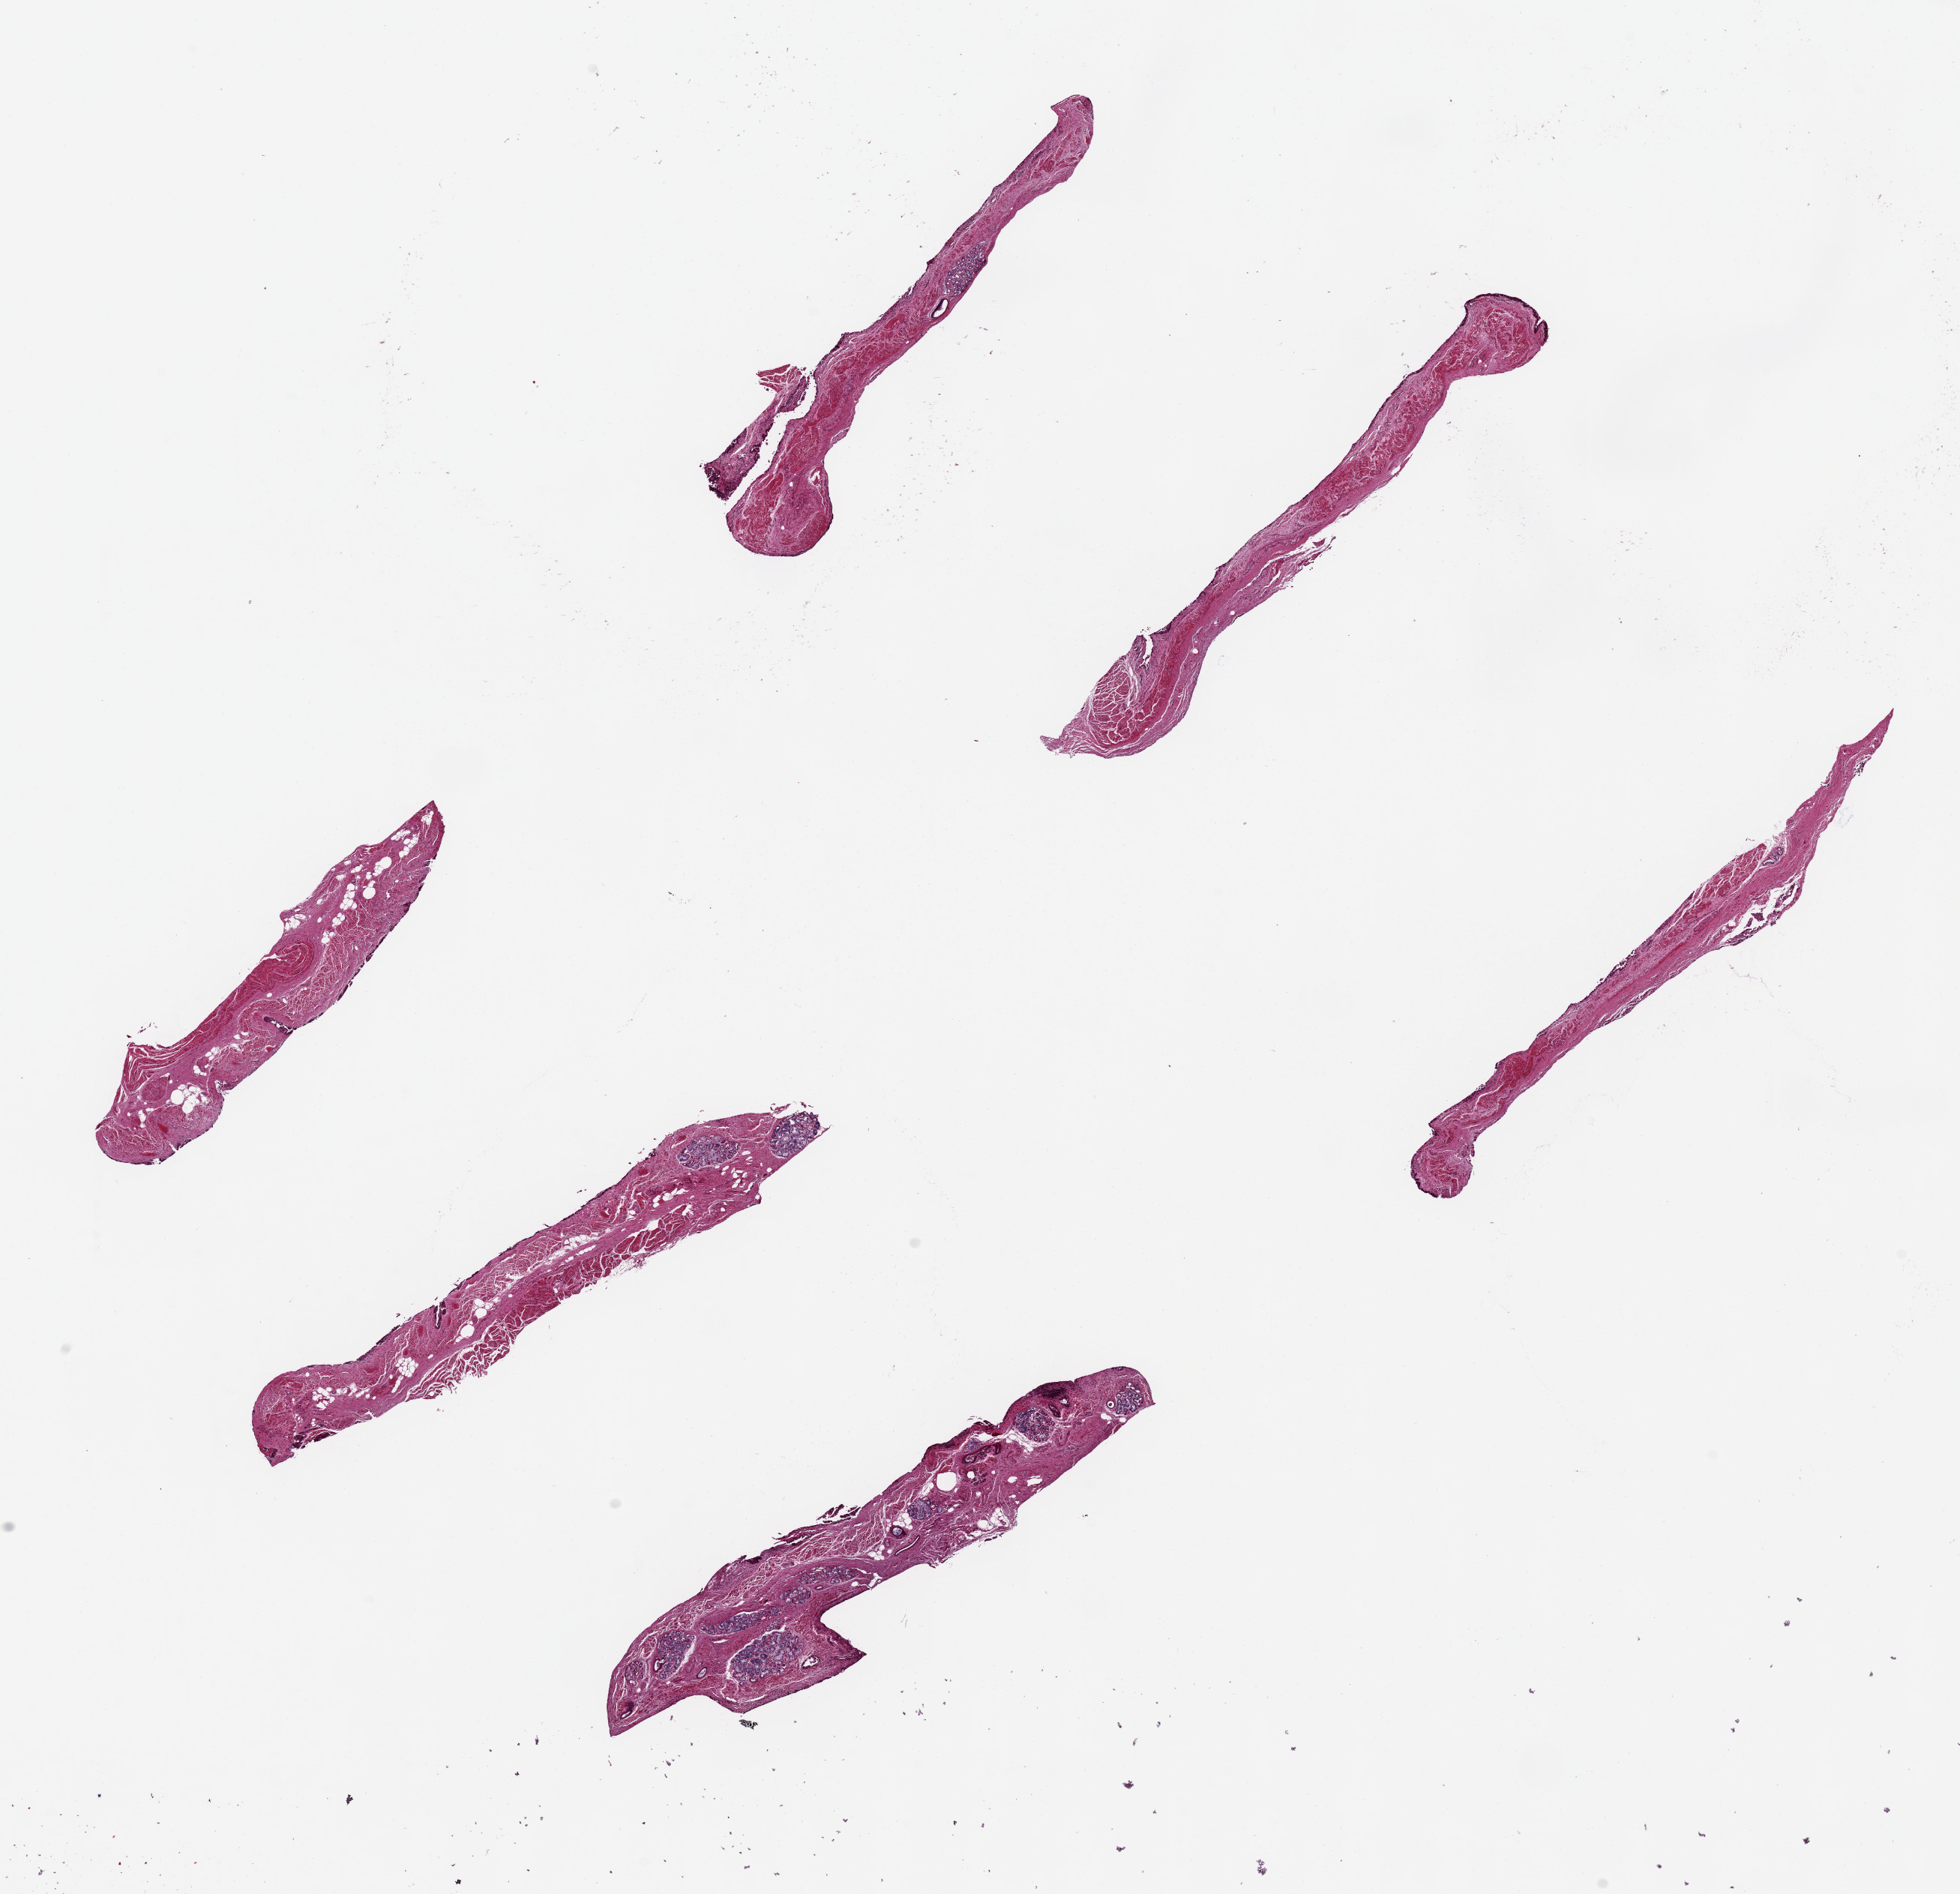
Whole-slide image, hematoxylin and eosin (H&E) stain, whole scanned area (about 20.7 x 20.0 mm, acquisition: 20x scan) shown as a low-resolution overview; PAXgene-fixed paraffin-embedded (PFPE) section; section of esophageal mucous membrane (target tissue); donor tissue sample. Donor: female.
* review note (as recorded): 6 pieces ~6x1mm, minimal squamous mucosa